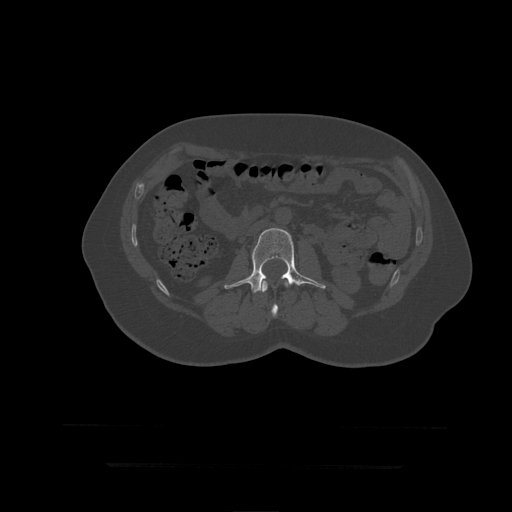
CT including the spine, one axial slice. Slice 129 of 399 in the series (ordered by position). Reconstruction kernel STANDARD. 120 kVp. Bone window (W 1800 / L 400 HU). 1.25 mm slice thickness. 512 × 512 image matrix, field of view 450 × 450 mm. Patient age 41 years. Case-level facts recorded for this patient, not image findings: primary cancer: breast.
Annotated regions visible in this slice (semi-automatic segmentation, software-assisted and operator-edited):
- L2 vertebra: bounding box (x1, y1, x2, y2) in pixels: (262, 281, 289, 318)
- L3 vertebra: (225, 228, 326, 294)